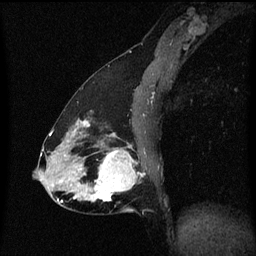
Breast MRI (dynamic contrast-enhanced), one sagittal slice. Slice 28 of 60 in the series (ordered by position). Dynamic contrast-enhanced series, image 2 of 3 at this slice position (ordered by acquisition). 1.5 T. TE 4.2 ms, TR 8.4 ms. 256 × 256 image matrix, field of view 200 × 200 mm. Female patient, age 47 years.
Annotated regions visible in this slice (semi-automatically segmented with operator editing):
- analysis volume of interest (the breast-tissue region the enhancement analysis was run in; not a lesion): bounding box (x1, y1, x2, y2) in pixels: (81, 138, 145, 213)
- tumour enhancement mask (voxels above the 70 % enhancement threshold inside the analysis volume of interest): (81, 148, 138, 203)